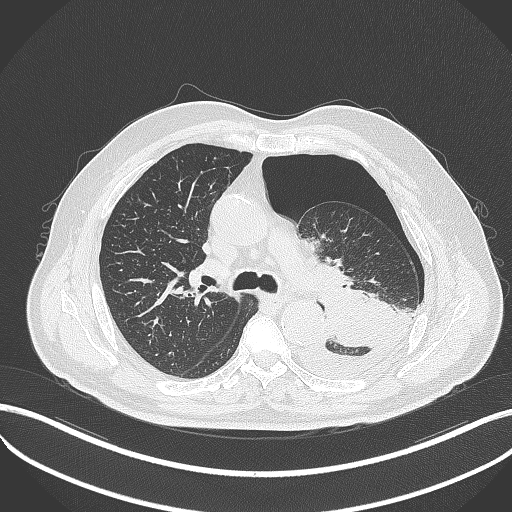
Chest CT, one axial slice. Position 334 of 464 along the scan axis. Lung window (W 1500 / L -600 HU). 1 mm slice thickness. 512 × 512 image matrix, field of view 400 × 400 mm. Patient: male, 76 years. From the clinical record (not read from this slice): clinical TNM (as recorded): T3 N0 M1b.
Structures marked on this image (rectangle marked by the reading radiologist):
- lung tumour (recorded histology: adenocarcinoma): bounding box <317,282,398,350> (left, top, right, bottom; pixels)